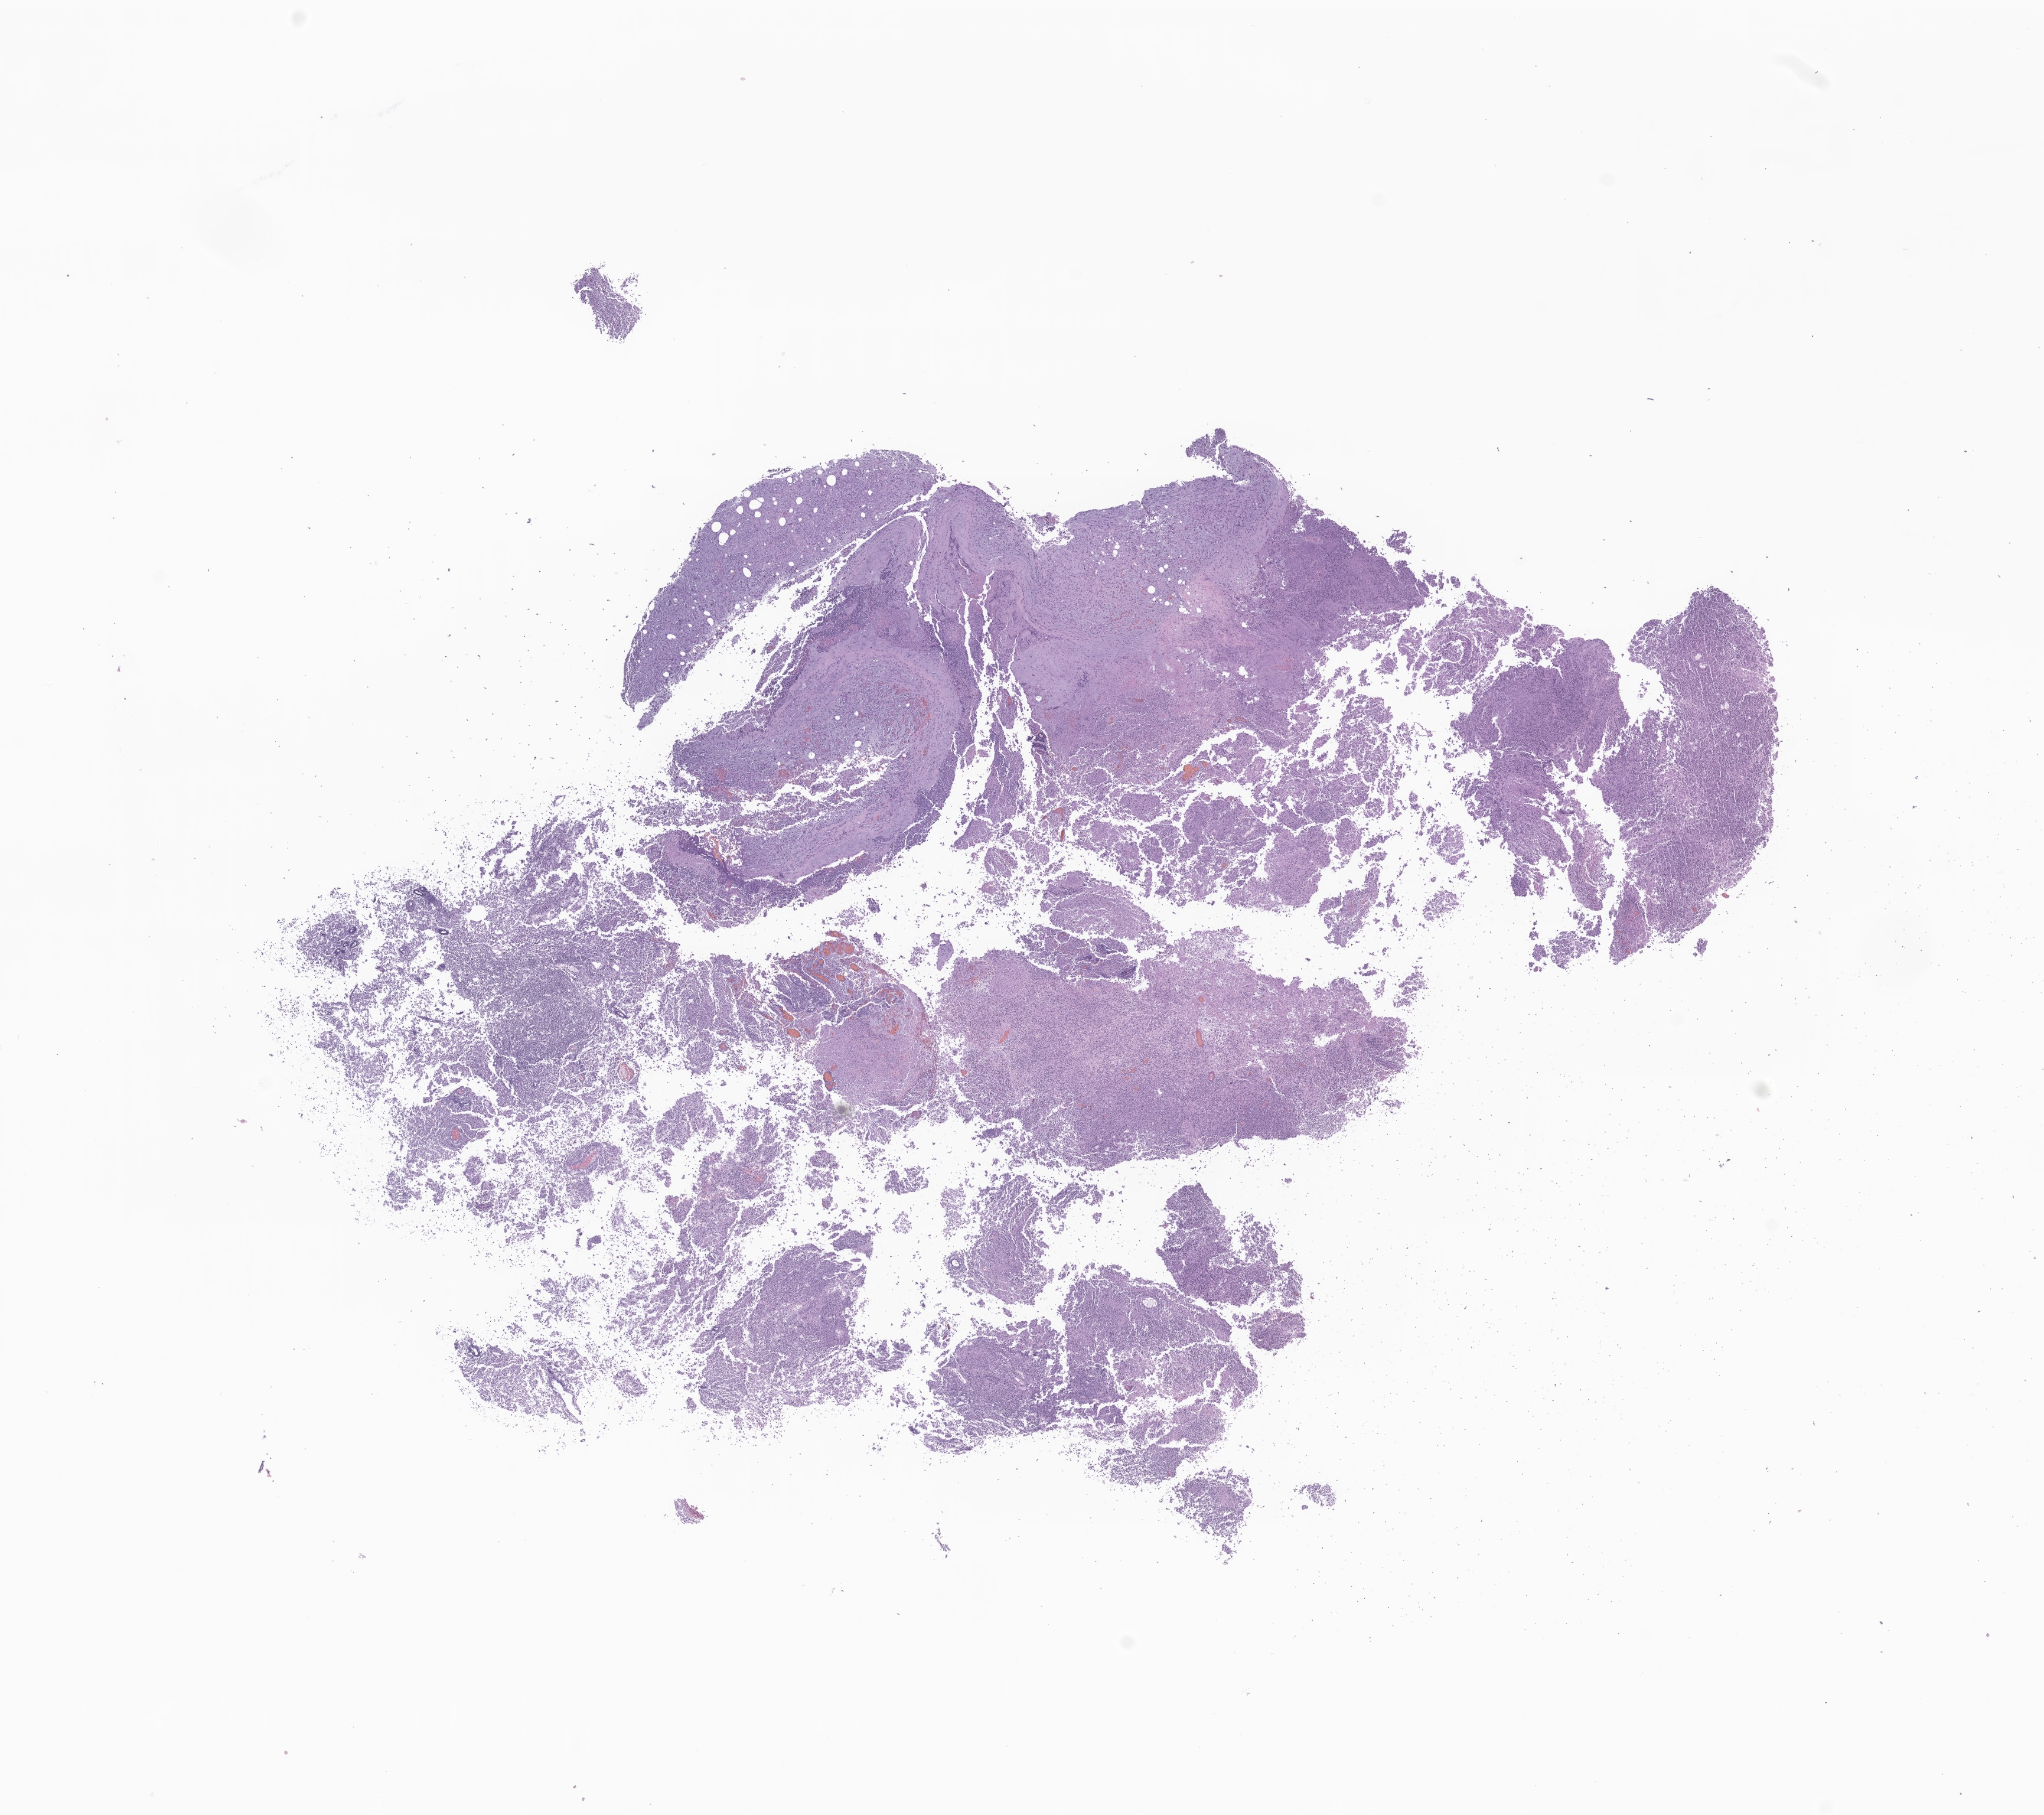
Whole-slide image, H&E stain of tumor tissue from the soft tissue of upper extremity — whole scanned area (about 14.6 x 13.0 mm) shown as a low-resolution overview. Formalin-fixed, paraffin-embedded (FFPE) tissue. Patient: male, age 177 months (14 years 9 months).
- tissue or organ of origin (case record): connective, subcutaneous and other soft tissues of upper limb and shoulder
- diagnosis (ICD-O-3 morphology term): Neuroblastoma, NOS